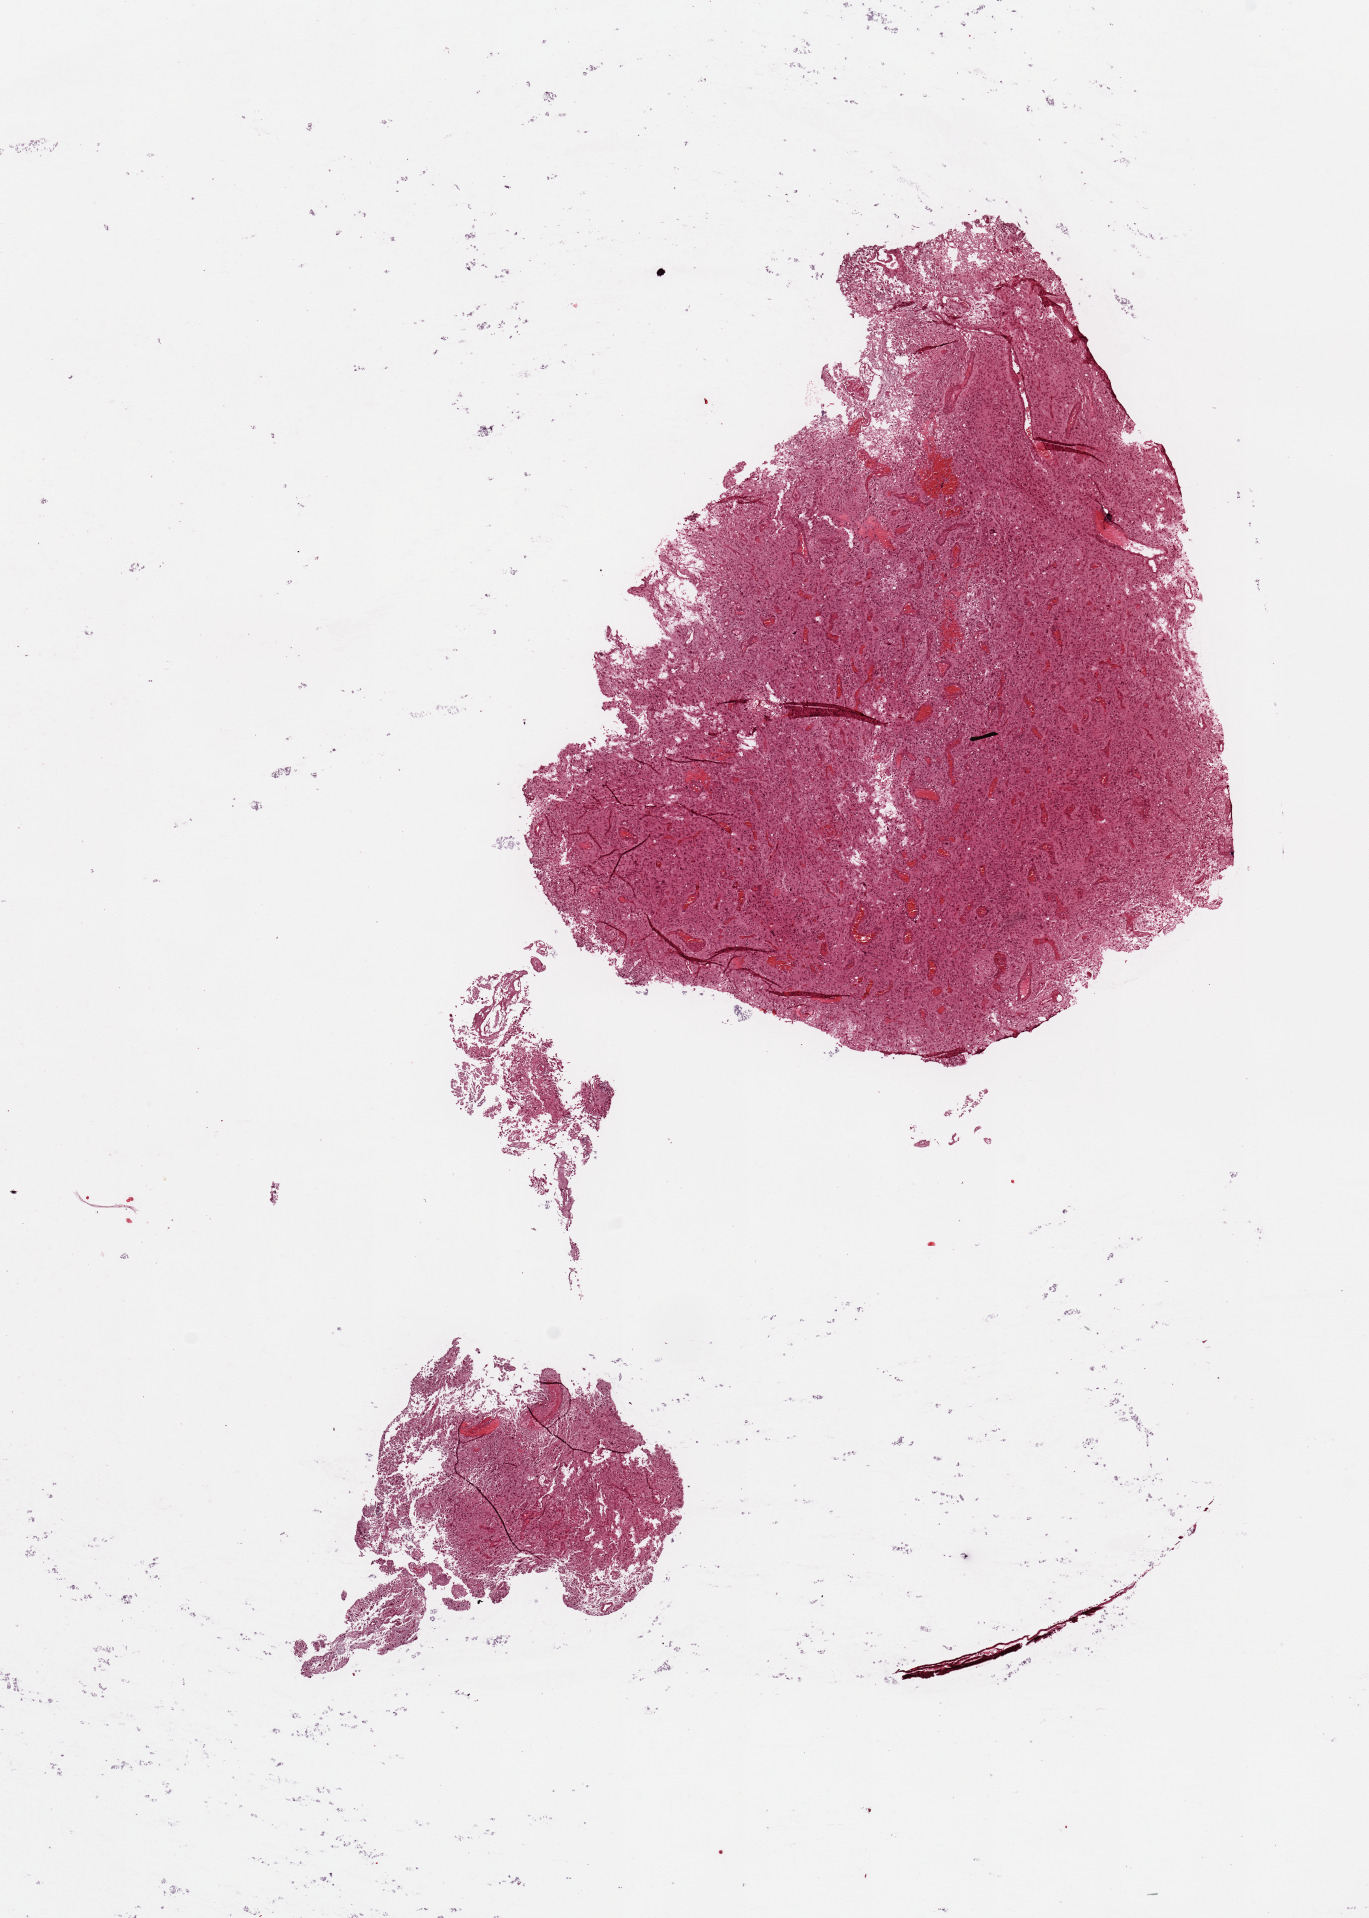
Whole-slide histology image, H&E, low-resolution overview of the scanned area, about 10.8 x 15.2 mm; tumour tissue sample, sampled site: brain. 60-year-old male patient. Composition of this section per pathologist review: tumour nuclei 80%, necrosis 5%.
- primary tumour site (as recorded): temporal lobe
- histologic diagnosis: Glioblastoma